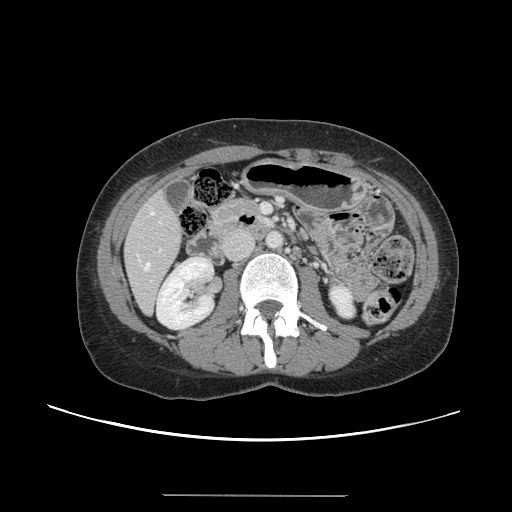
Contrast-enhanced abdominal CT, one axial slice. Slice 47 of 144 in the series (ordered by position). 120 kVp. Intravenous contrast given. Soft-tissue window (W 400 / L 40 HU). 512 × 512 image matrix, field of view 380 × 380 mm. Female patient, age 53 years. From the clinical record (not read from this slice): diagnosis: colorectal cancer liver metastases, imaged before liver resection; multiple liver metastases: yes; largest metastasis: 1.1 cm; chemotherapy before resection: no.
Structures marked on this image (manually delineated by an expert):
- hepatic veins: bounding box (x1, y1, x2, y2) in pixels: (145, 212, 154, 269)
- liver: (125, 194, 182, 313)
- planned liver remnant (the part of the liver to remain after resection): (126, 194, 183, 313)
- portal vein (with intrahepatic branches): (150, 248, 162, 282)